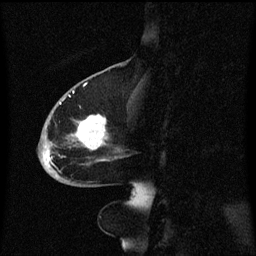
Breast MRI (dynamic contrast-enhanced), one sagittal slice. Slice 25 of 60 in the series (ordered by position). Dynamic contrast-enhanced series, image 2 of 3 at this slice position (ordered by acquisition). 1.5 T. TE 4.2 ms, TR 8.4 ms. 2 mm slice thickness. 256 × 256 image matrix, field of view 200 × 200 mm. Female patient, age 68 years. From the clinical record (not read from this slice): setting: breast cancer imaged before/during neoadjuvant chemotherapy; receptor status: triple-negative.
Structures marked on this image (semi-automatically segmented with operator editing):
- analysis volume of interest (the breast-tissue region the enhancement analysis was run in; not a lesion): bounding box [x1, y1, x2, y2] px = [39, 94, 130, 173]
- tumour enhancement mask (voxels above the 70 % enhancement threshold inside the analysis volume of interest): [44, 102, 109, 169]